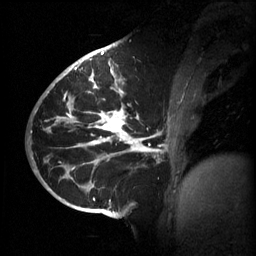
Breast MRI (dynamic contrast-enhanced), one sagittal slice. Slice 29 of 60 in the series (ordered by position). 3 images stored at this slice position (order not interpretable as contrast timing). 1.5 T. TE 4.2 ms, TR 11 ms. 2 mm slice thickness. 256 × 256 image matrix, field of view 220 × 220 mm. Patient: female, 51 years.
Outlined on this slice (semi-automatically segmented with operator editing):
- analysis volume of interest (the breast-tissue region the enhancement analysis was run in; not a lesion): bounding box [x1, y1, x2, y2] px = [63, 80, 187, 201]
- tumour enhancement mask (voxels above the 70 % enhancement threshold inside the analysis volume of interest): [63, 80, 166, 201]